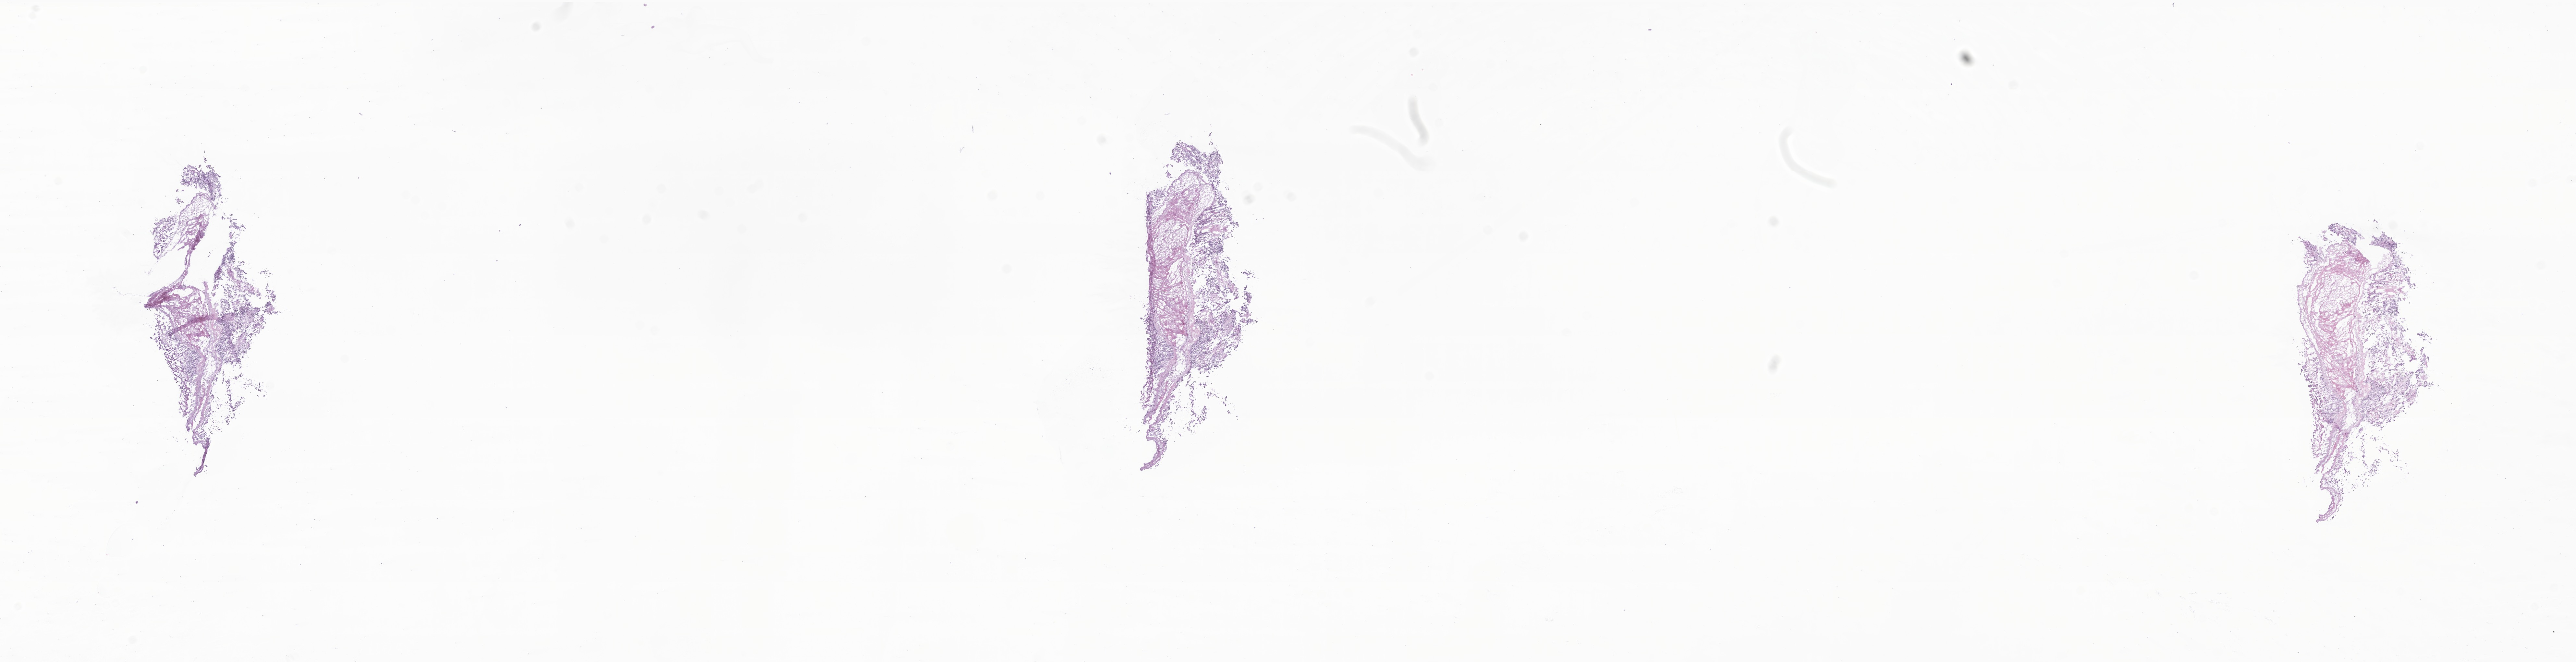
Digitized hematoxylin and eosin (H&E)-stained section of tumor tissue from the frontal lobe — whole scanned area (about 33.5 x 8.6 mm) shown as a low-resolution overview. Frozen section. Patient female; age 114 months.
- recorded diagnosis: Glioma, malignant